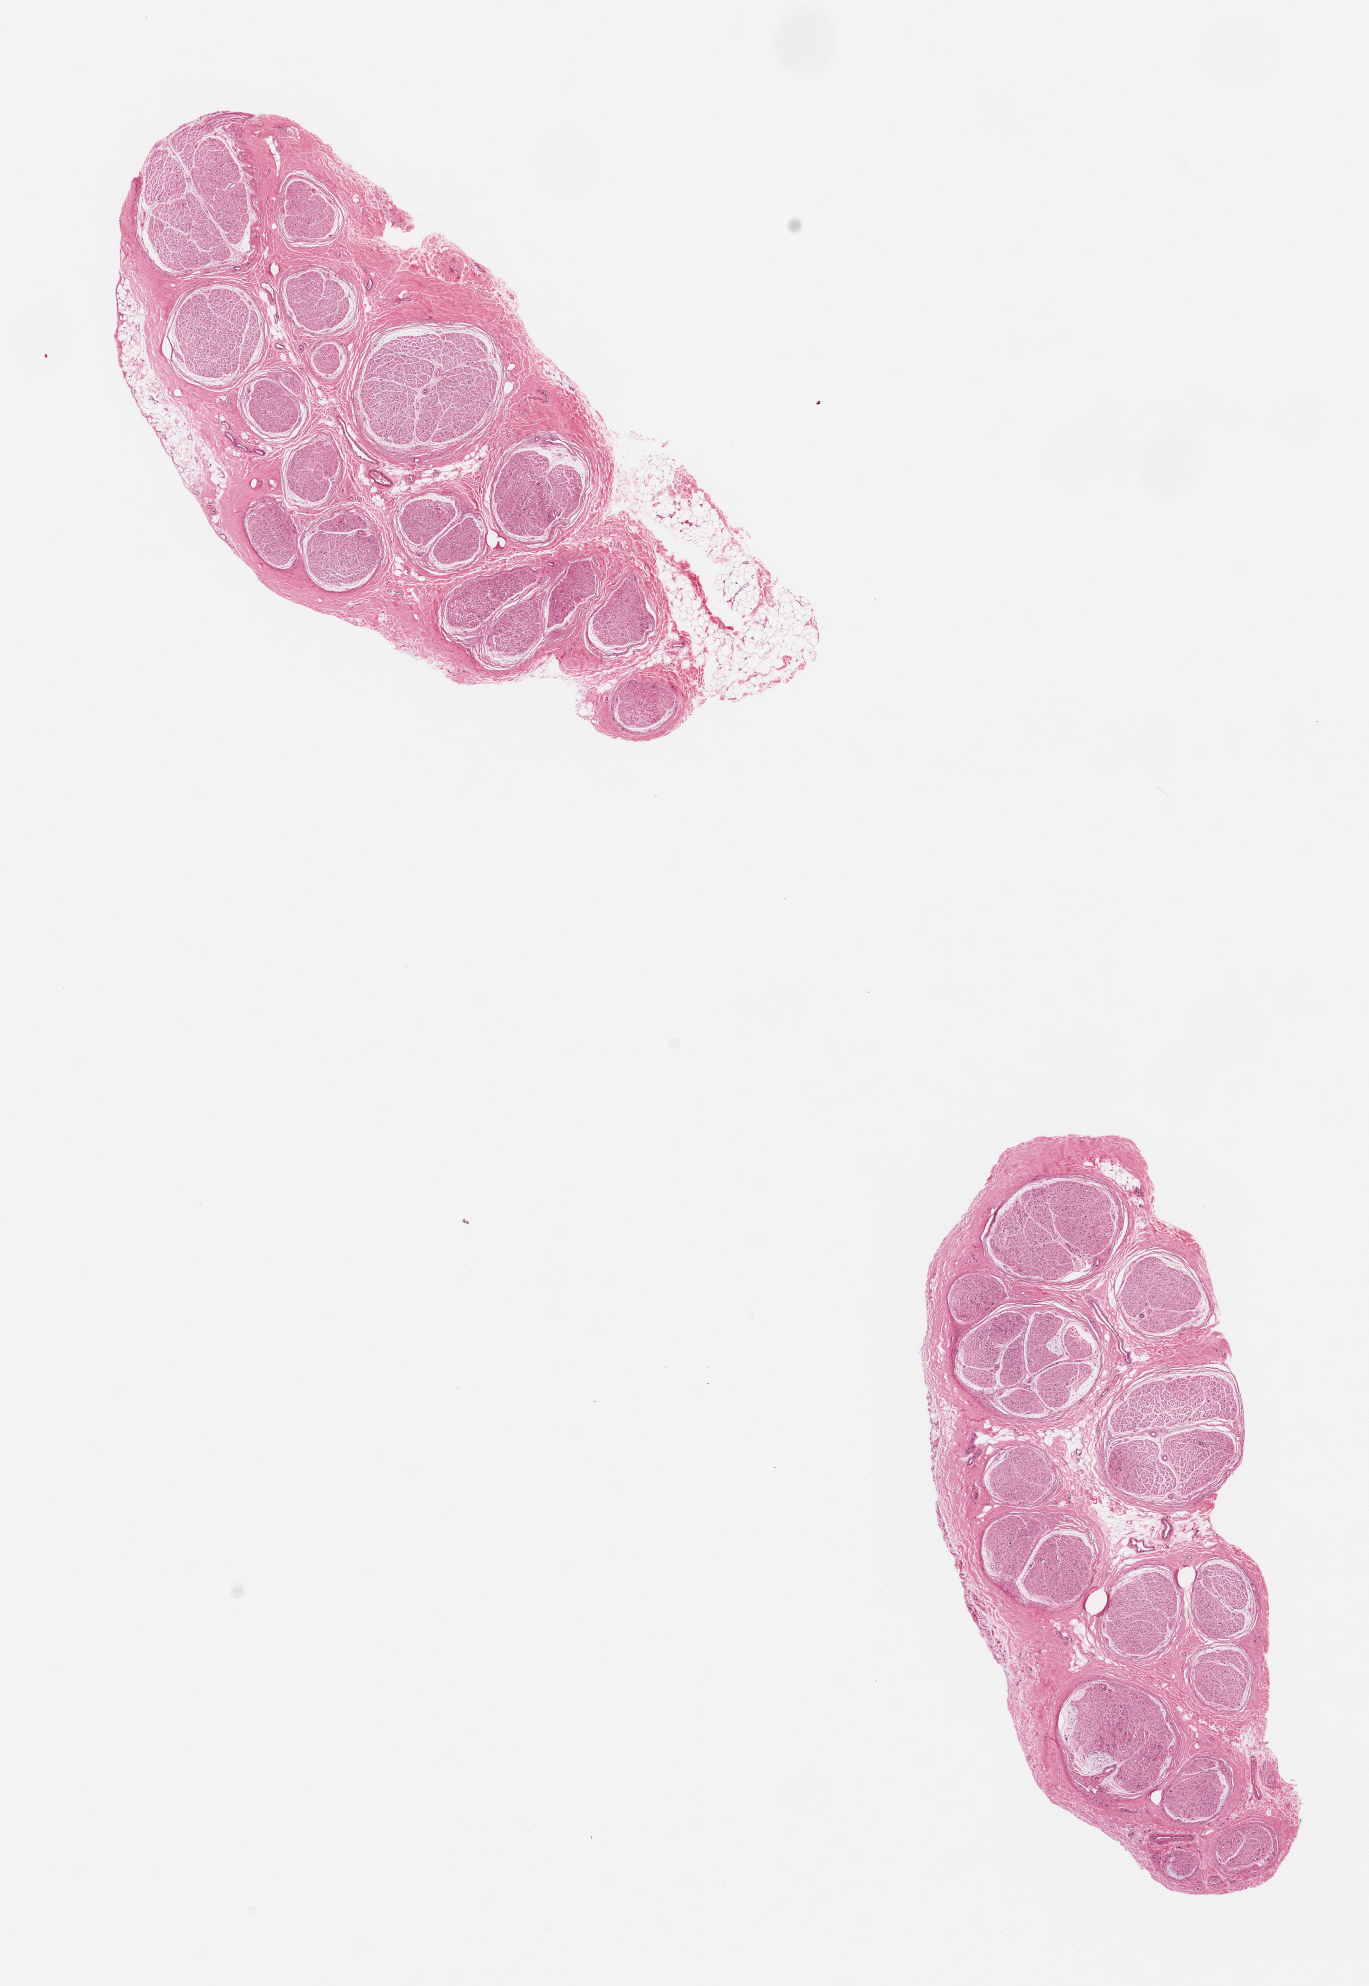
Digitized haematoxylin and eosin-stained section, a low-resolution overview of the entire scanned area, about 10.8 x 15.7 mm (acquisition: 20x scan), PAXgene-fixed, paraffin-embedded tissue, target tissue: tibial nerve, tissue donor sample. Male donor.
• reviewer comment on this tissue sample: 2 pieces, single nubbin adherent fat, ~1.4mm